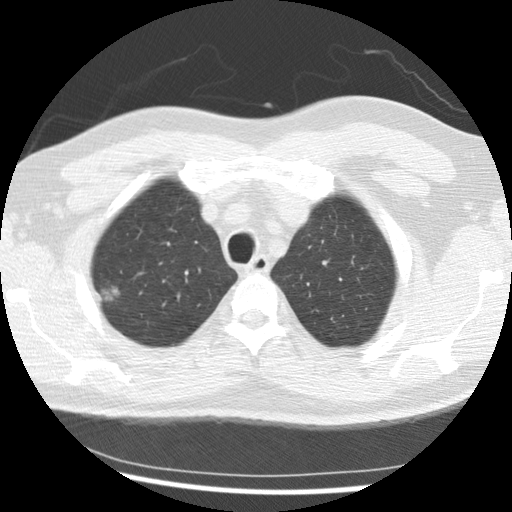
Chest CT (low-dose screening protocol), one axial image; baseline screening round; lung window (W 1500 / L -600 HU); 2.5 mm slice thickness; slice 47 of 265 in the series; 512 × 512 image matrix. Male, age 56 years at enrolment.
Lesion marked by an expert reader, bounding box (x1, y1, x2, y2) in pixels: (85, 274, 133, 315). Reader record for this screening exam (exam-level; its link to the box is not recorded): non-calcified nodule or mass ≥4 mm, right upper lobe, 19 × 15 mm, spiculated (stellate) margins, soft tissue attenuation. Later outcome: lung cancer diagnosed 291 days after this screen — non-small cell carcinoma, right upper lobe, poorly differentiated (G3), stage IIIB (AJCC 6th edition), 20 mm at pathology.